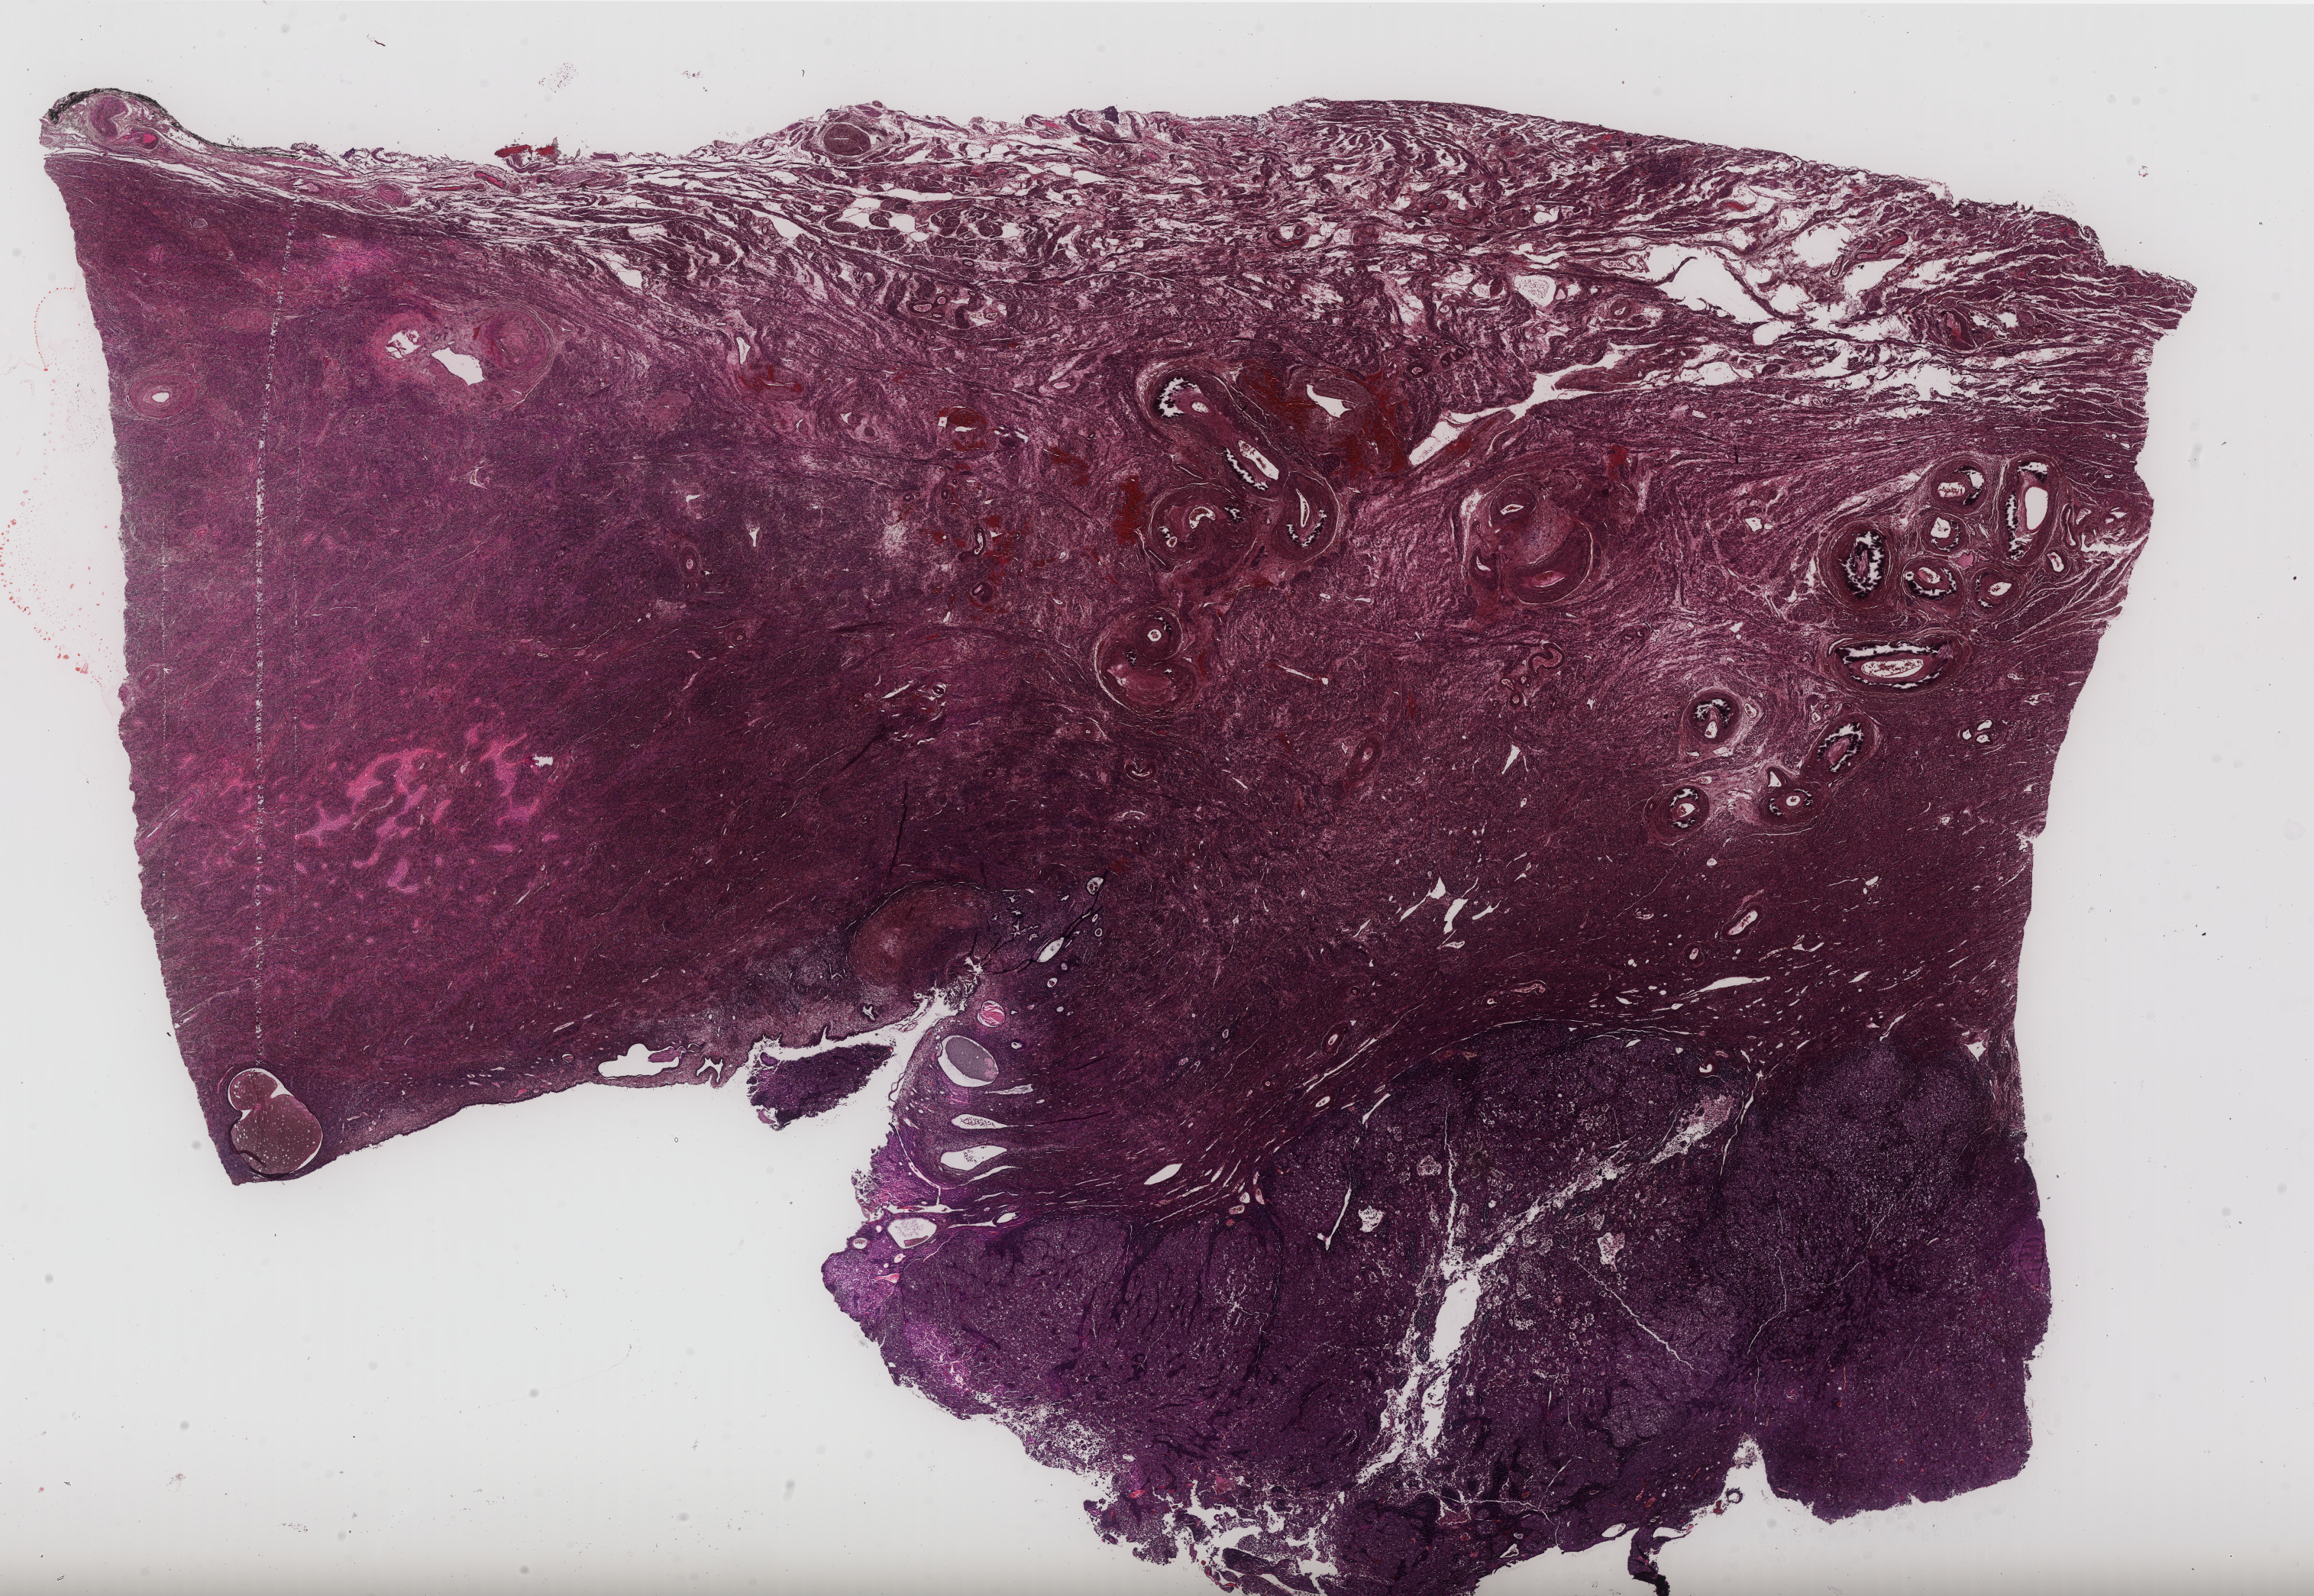
Hematoxylin and eosin (H&E) stained whole-slide image — whole scanned area (about 24.3 x 16.8 mm, acquisition: 40x scan) shown as a low-resolution overview, formalin-fixed paraffin-embedded (FFPE) diagnostic section, sample: primary tumour, uterus. Female, age 73 years at initial diagnosis. Histologic grade: G3 (poorly differentiated).
- FIGO stage: IB
- diagnosis: Clear cell adenocarcinoma, NOS (endometrium)
- lymph nodes positive (case pathology): 0 of 21 examined